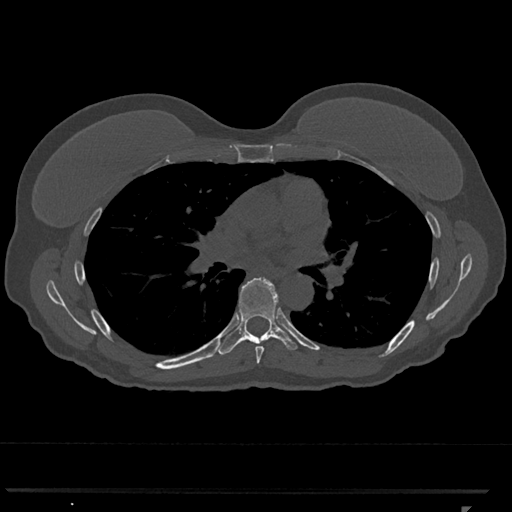
CT including the spine, one axial slice. 120 kVp. Bone window (W 1800 / L 400 HU). 0.5 mm slice thickness. 512 × 512 image matrix. Female patient, age 62 years. From the clinical record (not read from this slice): primary cancer: renal.
Annotated regions visible in this slice (semi-automatically segmented with operator editing):
- T6 vertebra: bounding box [x1, y1, x2, y2] px = [255, 343, 264, 364]
- T7 vertebra: [216, 278, 298, 355]